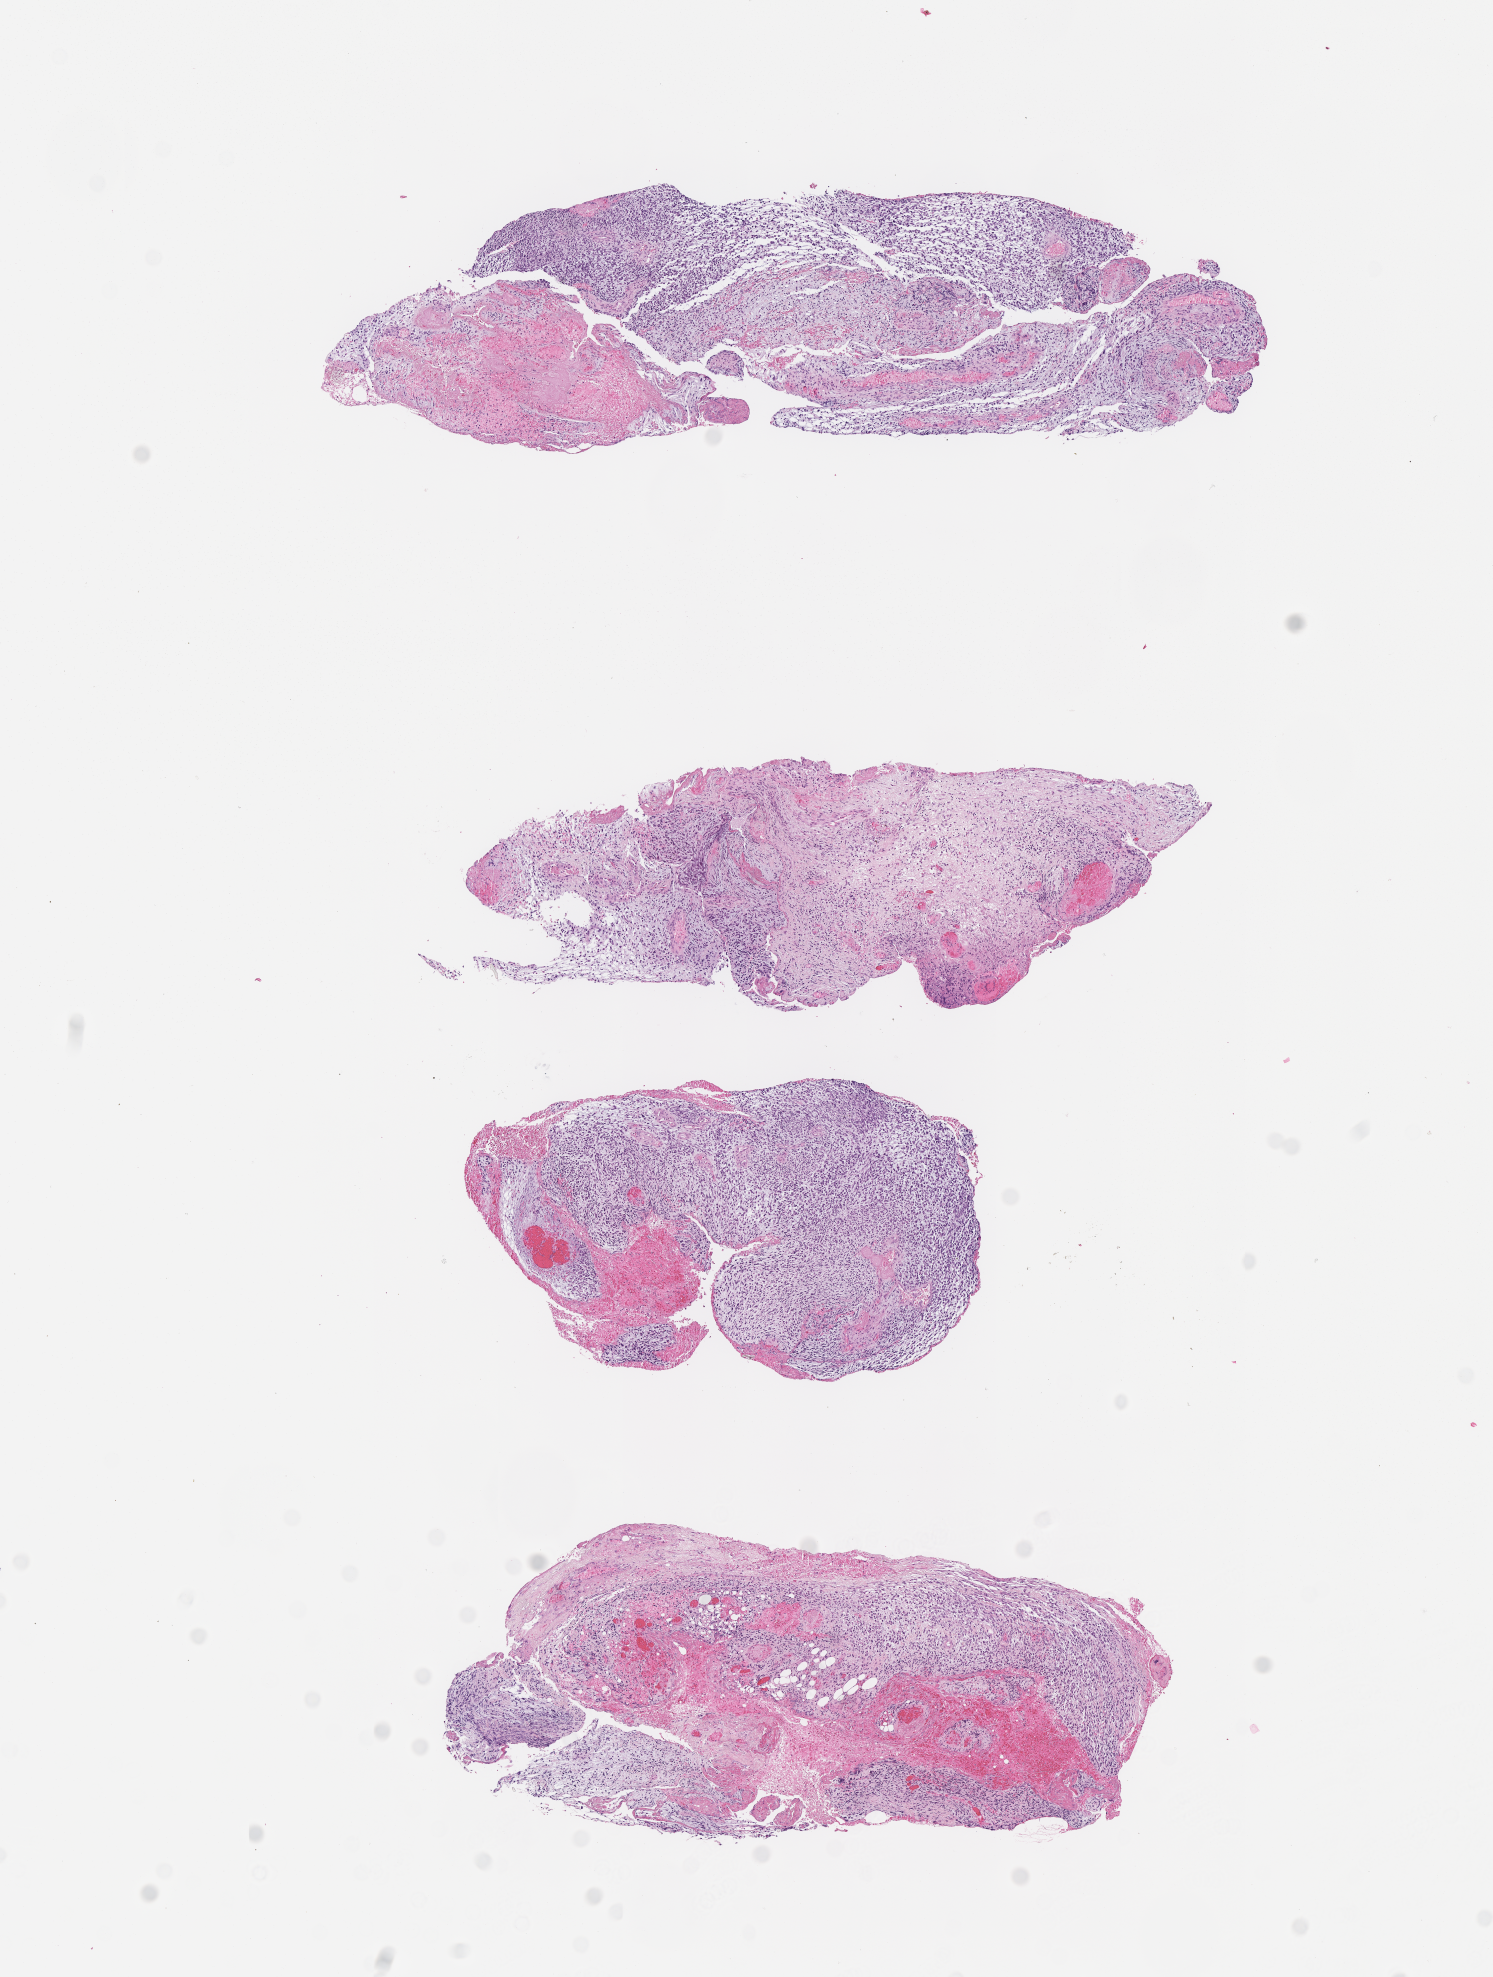
Hematoxylin and eosin (H&E) whole-slide image of tumor tissue, low-resolution overview of the scanned area, about 6.0 x 8.0 mm. FFPE section. Site: orbit, right. Patient: male, age 2.7 years at diagnosis.
Diagnosis: rhabdomyosarcoma; histological classification: embryonal rhabdomyosarcoma.